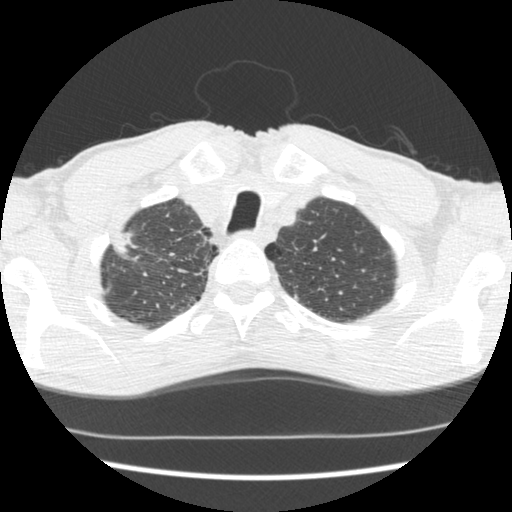
Axial slice from a low-dose chest CT screening exam. Baseline annual screen. Lung window (W 1500 / L -600 HU). Slice 31 of 197 in the series. 512 × 512 image matrix. Male participant, aged 62 years at enrolment. Current smoker at enrolment.
Lesion marked by an expert reader, box from (x=96, y=224) to (x=147, y=273) px. Screening reader's record for this exam: no non-calcified nodule ≥4 mm recorded. Official screen result: negative screen, significant abnormalities not suspicious for lung cancer.